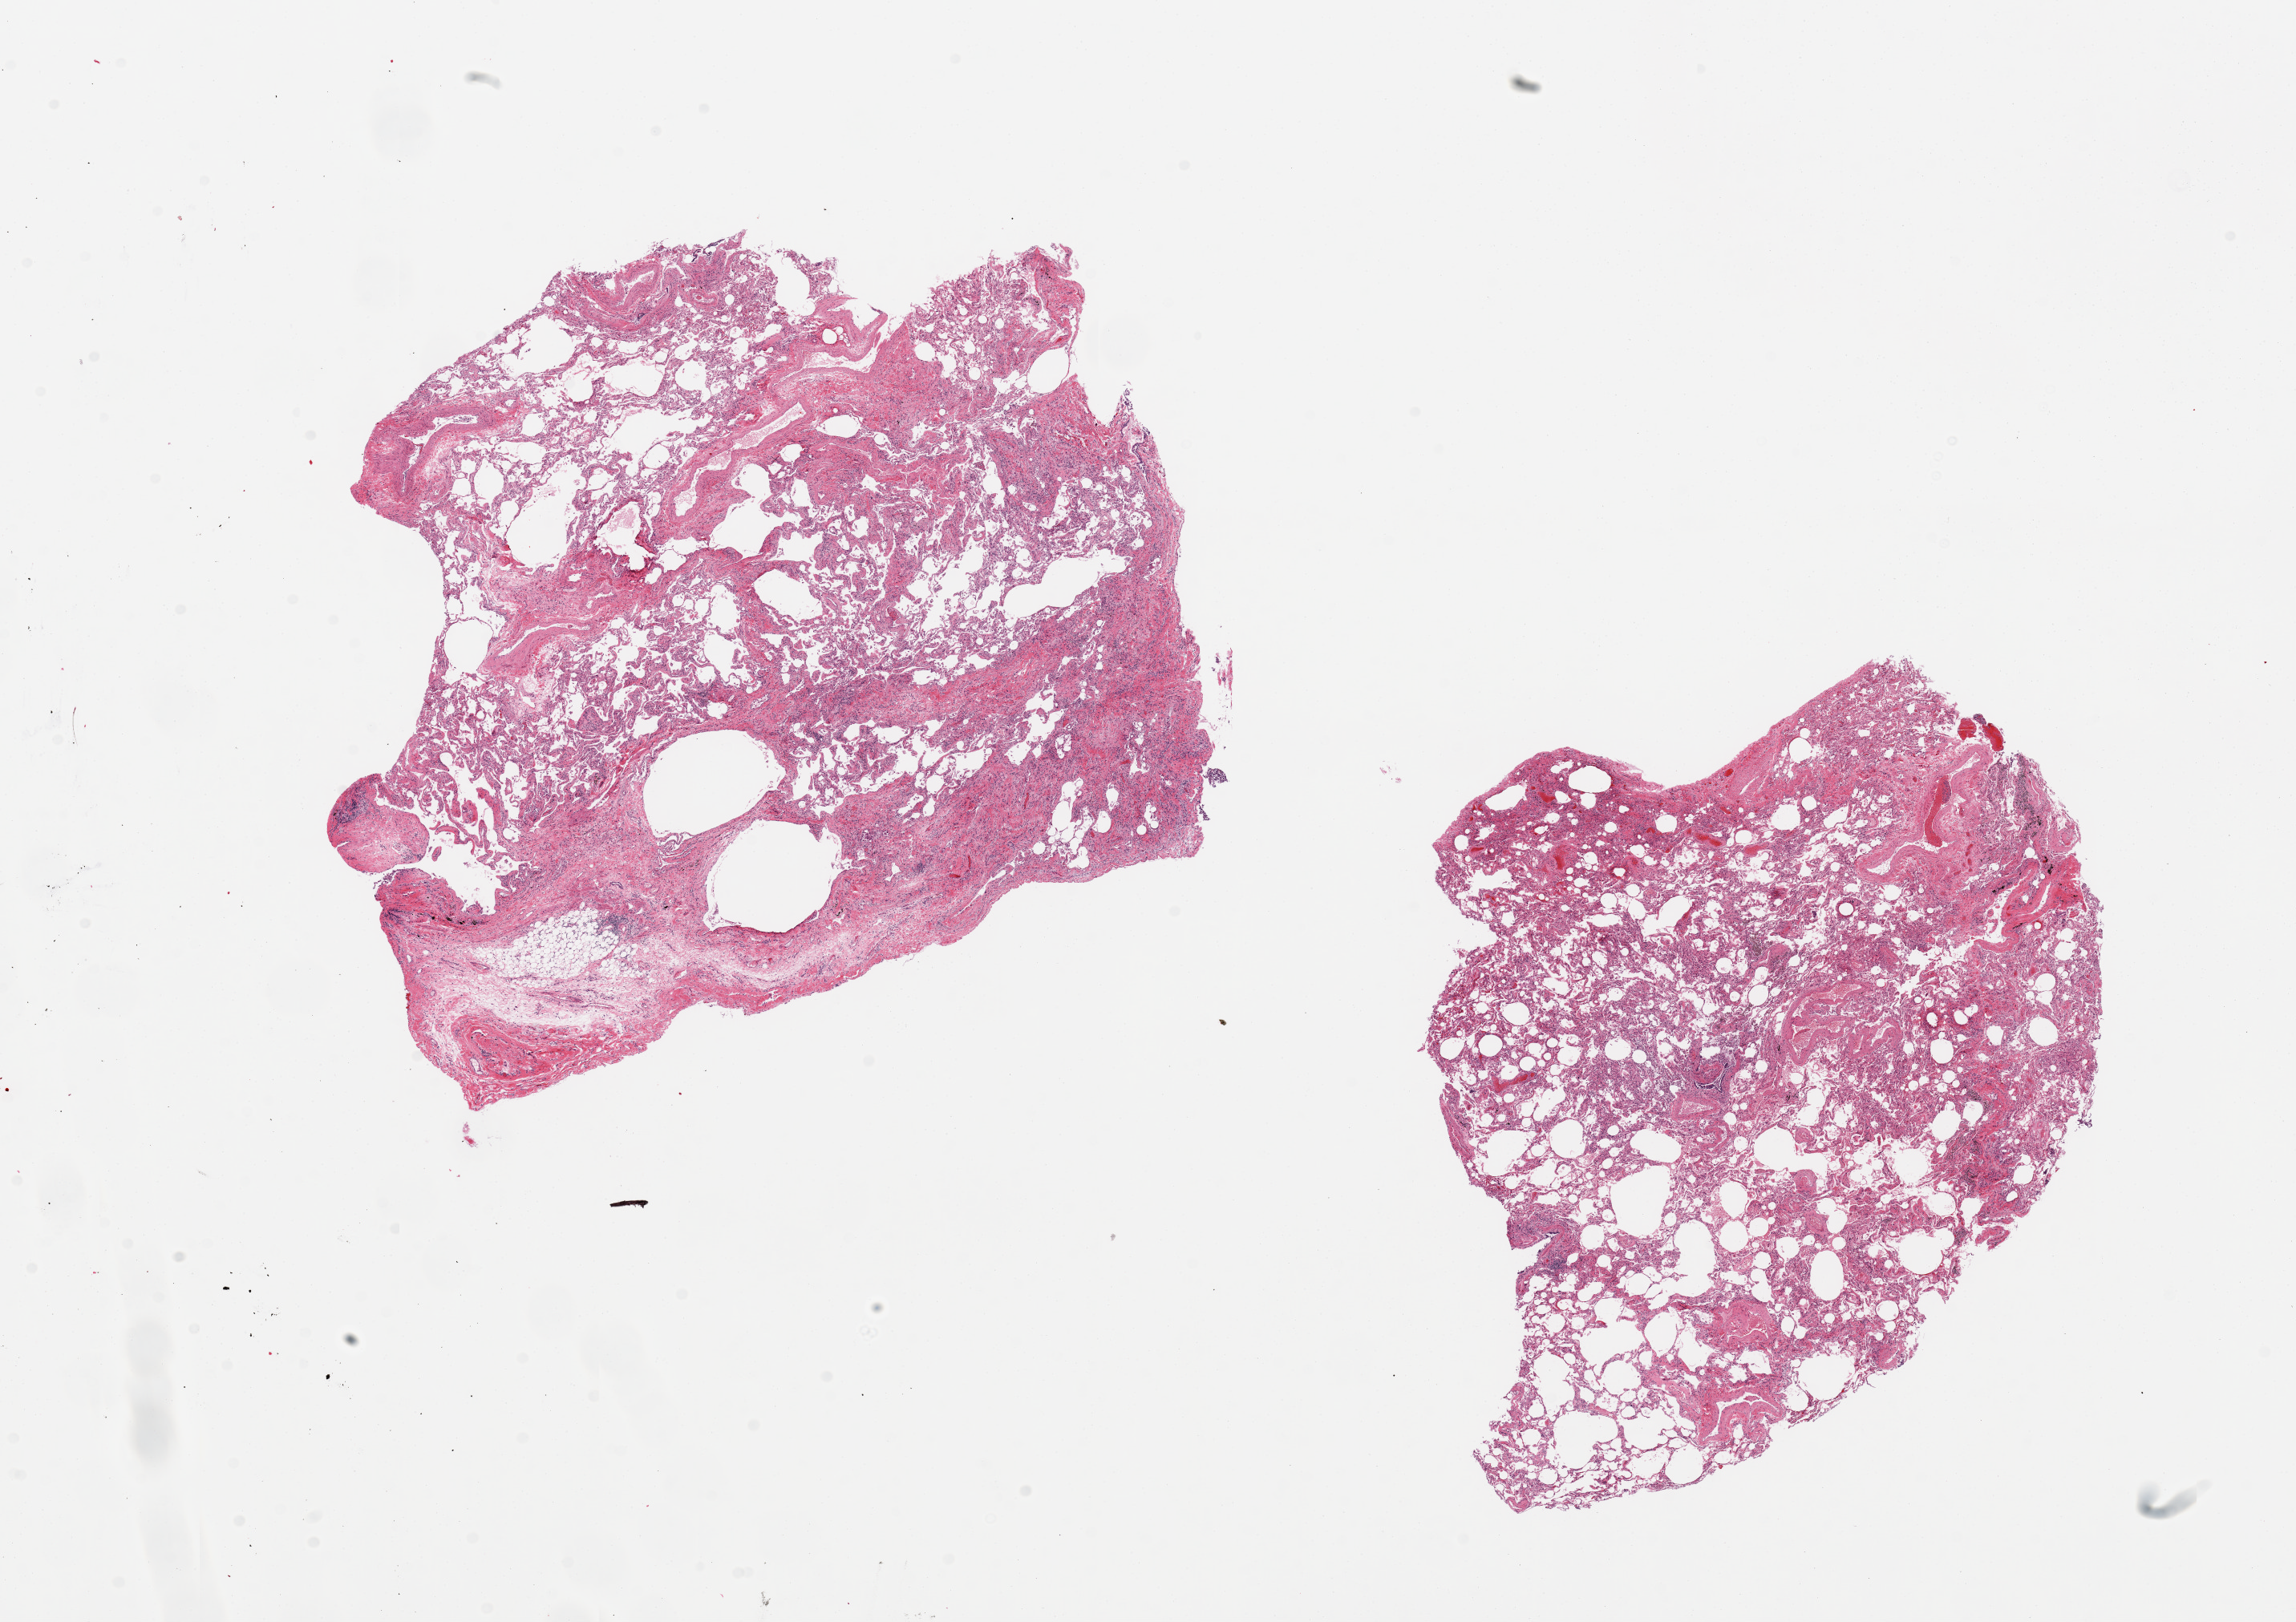
Whole-slide image, haematoxylin and eosin stain, whole scanned area (about 22.6 x 16.0 mm, from a 20x scan) shown as a low-resolution overview. PAXgene-fixed, paraffin-embedded tissue. Section of lung (target tissue). Tissue donor sample. Donor: male.
Reviewer comment on this tissue sample: 2 pieces; emphysema and fibrosis; patchy bronchopneumonia.